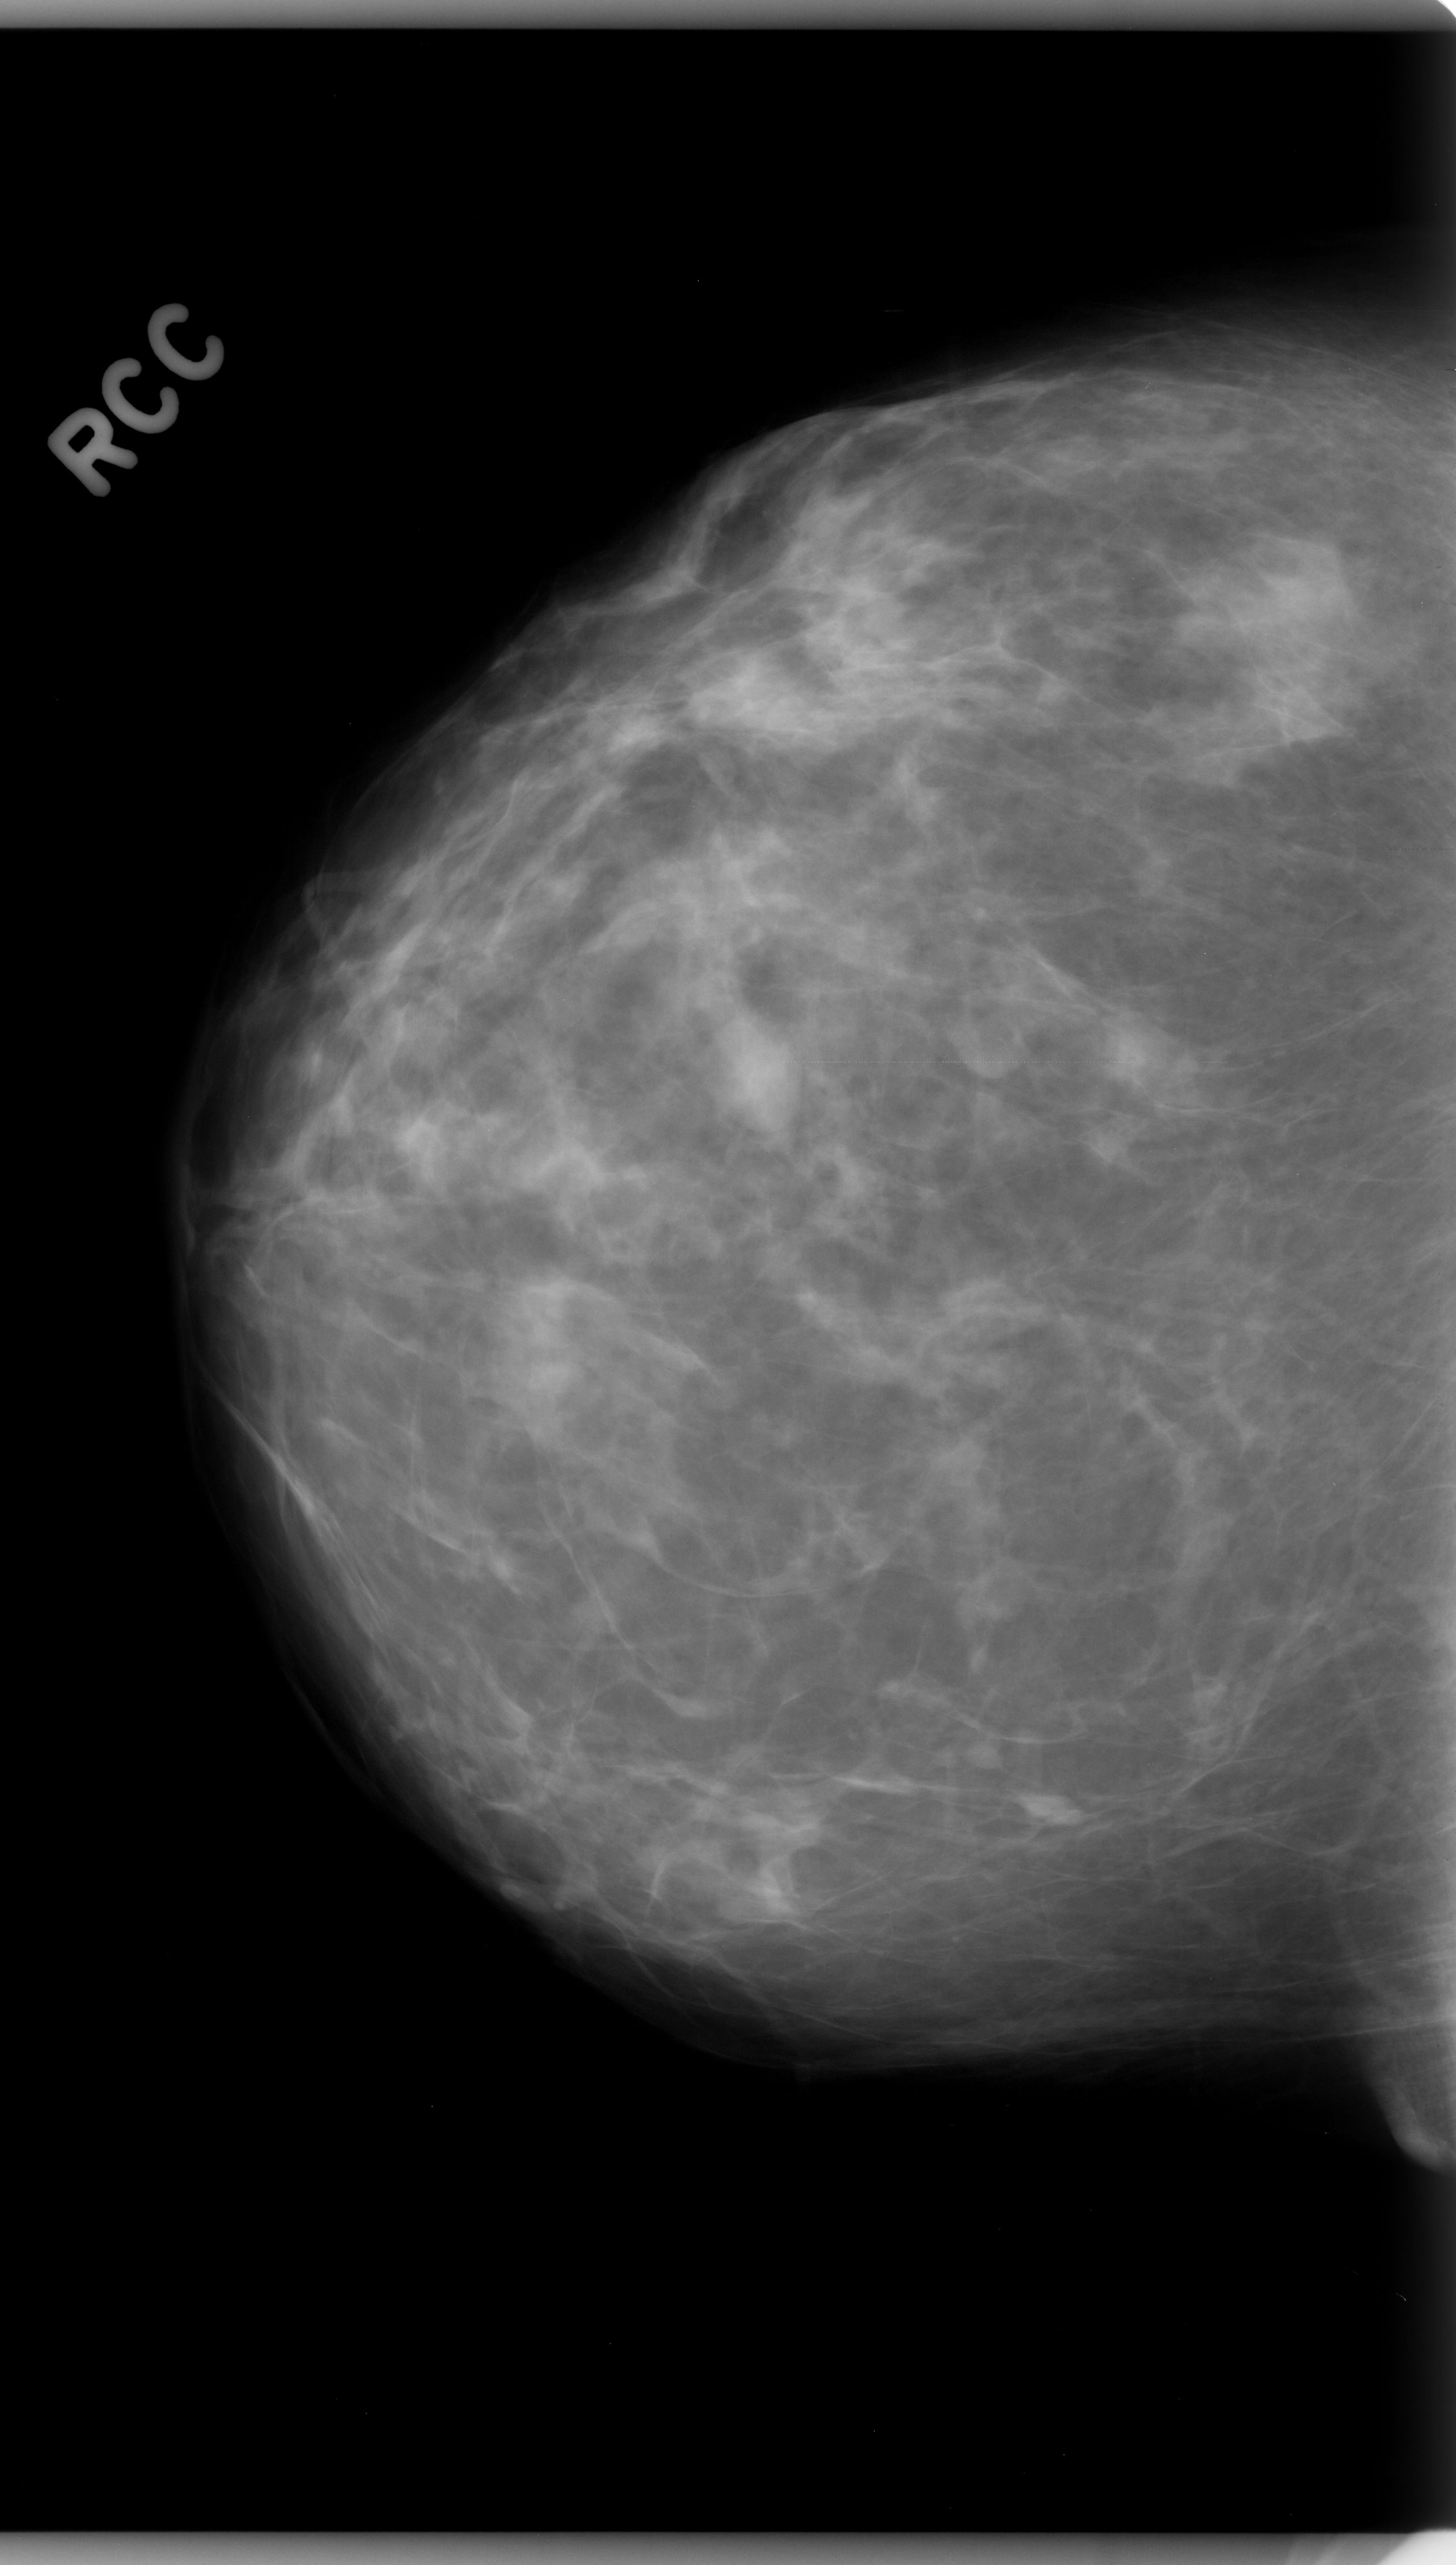
Mammogram (digitized film), right breast, craniocaudal (CC) view, breast composition: scattered fibroglandular densities (BI-RADS density category 2 of 4).
- Finding: mass, shape oval, margins obscured; BI-RADS assessment category 3; subtlety rating 4 on a 1 (subtle) to 5 (obvious) scale; pathology result (as recorded, not read from the image): benign.